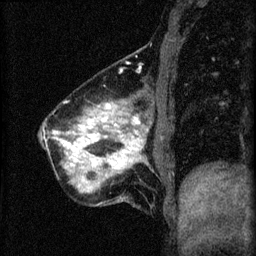
Breast MRI (dynamic contrast-enhanced), one sagittal slice. Position 16 of 60 along the scan axis. 3 images stored at this slice position (order not interpretable as contrast timing). 1.5 T. TE 4.2 ms, TR 8.2 ms. 256 × 256 image matrix, field of view 180 × 180 mm. Patient: female, 40 years.
Structures marked on this image (semi-automatic segmentation, software-assisted and operator-edited):
- analysis volume of interest (the breast-tissue region the enhancement analysis was run in; not a lesion): bounding box (x1, y1, x2, y2) in pixels: (42, 92, 171, 207)
- tumour enhancement mask (voxels above the 70 % enhancement threshold inside the analysis volume of interest): (54, 104, 143, 171)